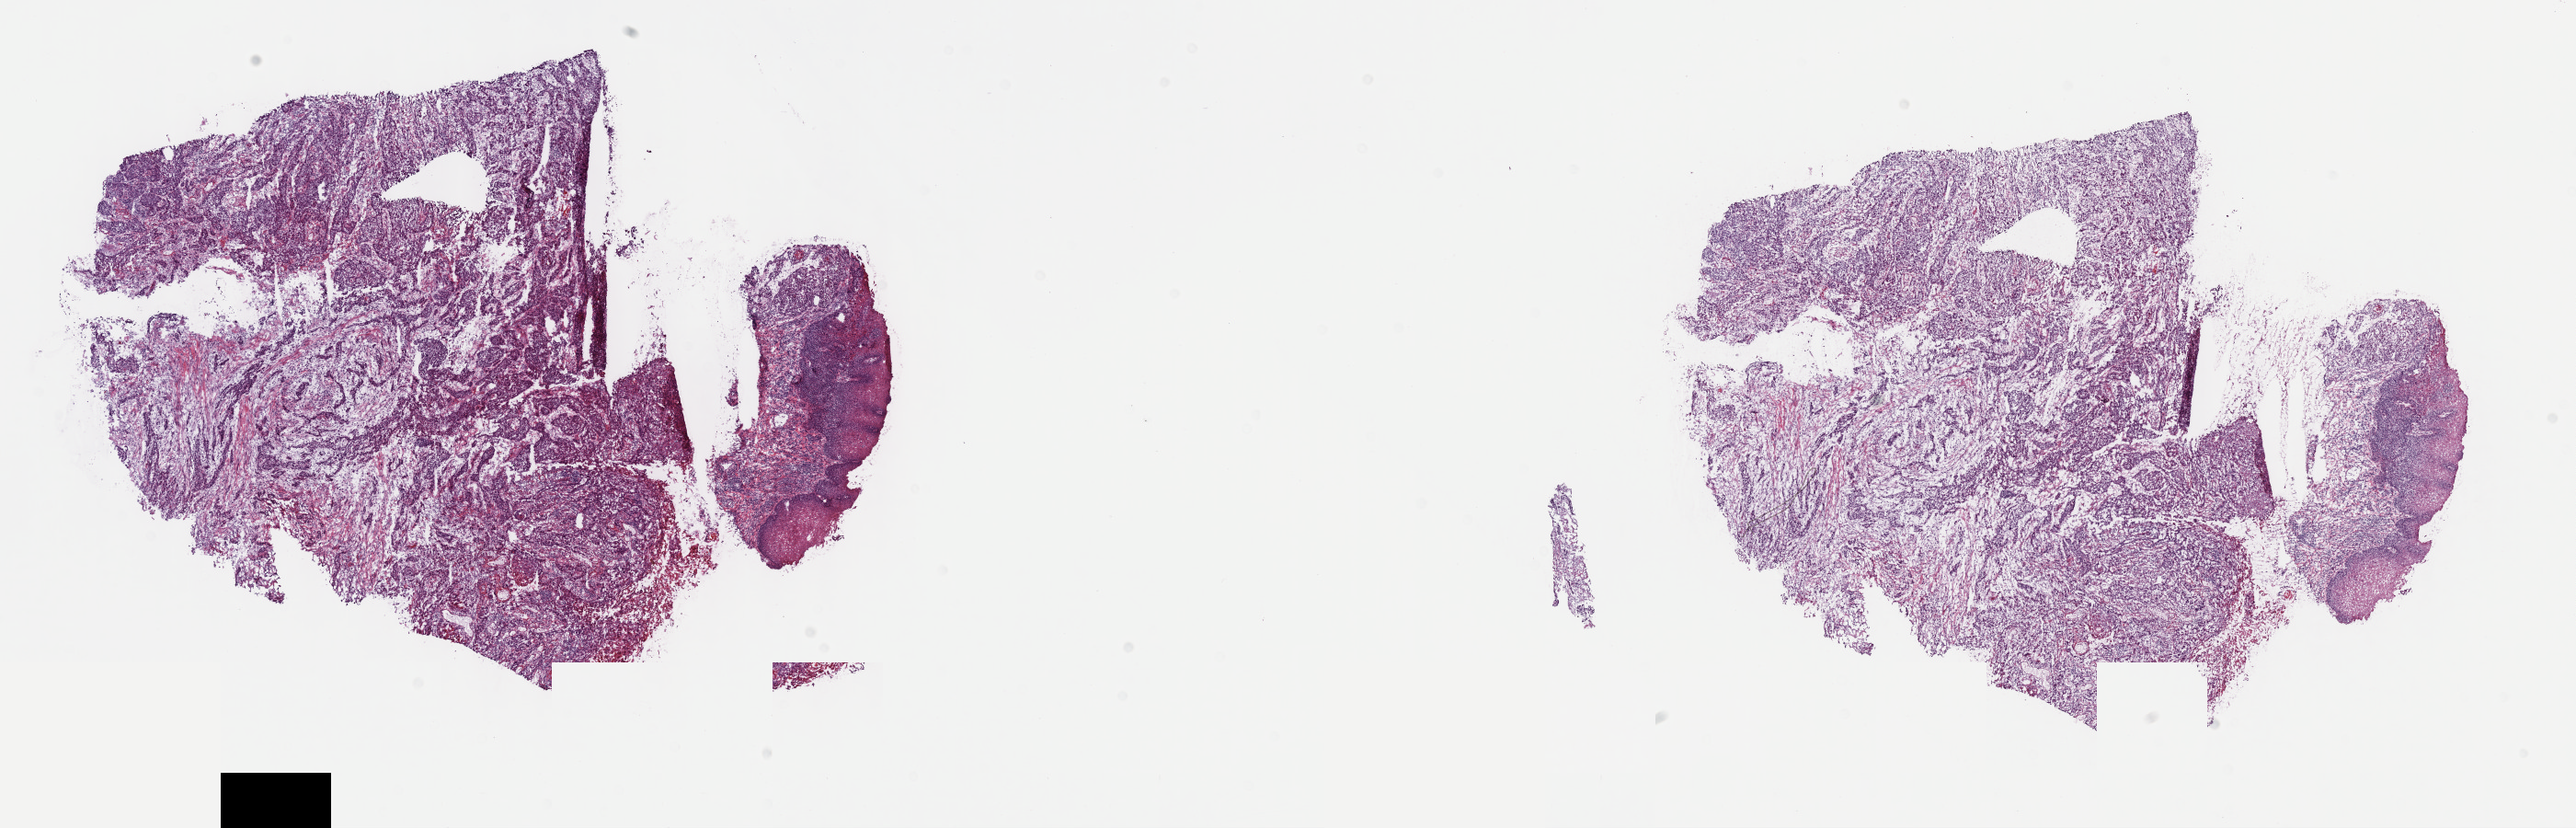
Whole-slide histology image, Hematoxylin and eosin (H&E) stained — a low-resolution overview of the entire scanned area, about 22.7 x 7.3 mm (from a 40x scan). Frozen section from the top of the tissue portion. Esophagus, primary tumour sample. Female patient; age at initial diagnosis 51 years. Slide review estimates, as recorded: tumour cells 50%, tumour nuclei 80%.
Pathologic diagnosis: Squamous cell carcinoma, NOS (middle third of esophagus).